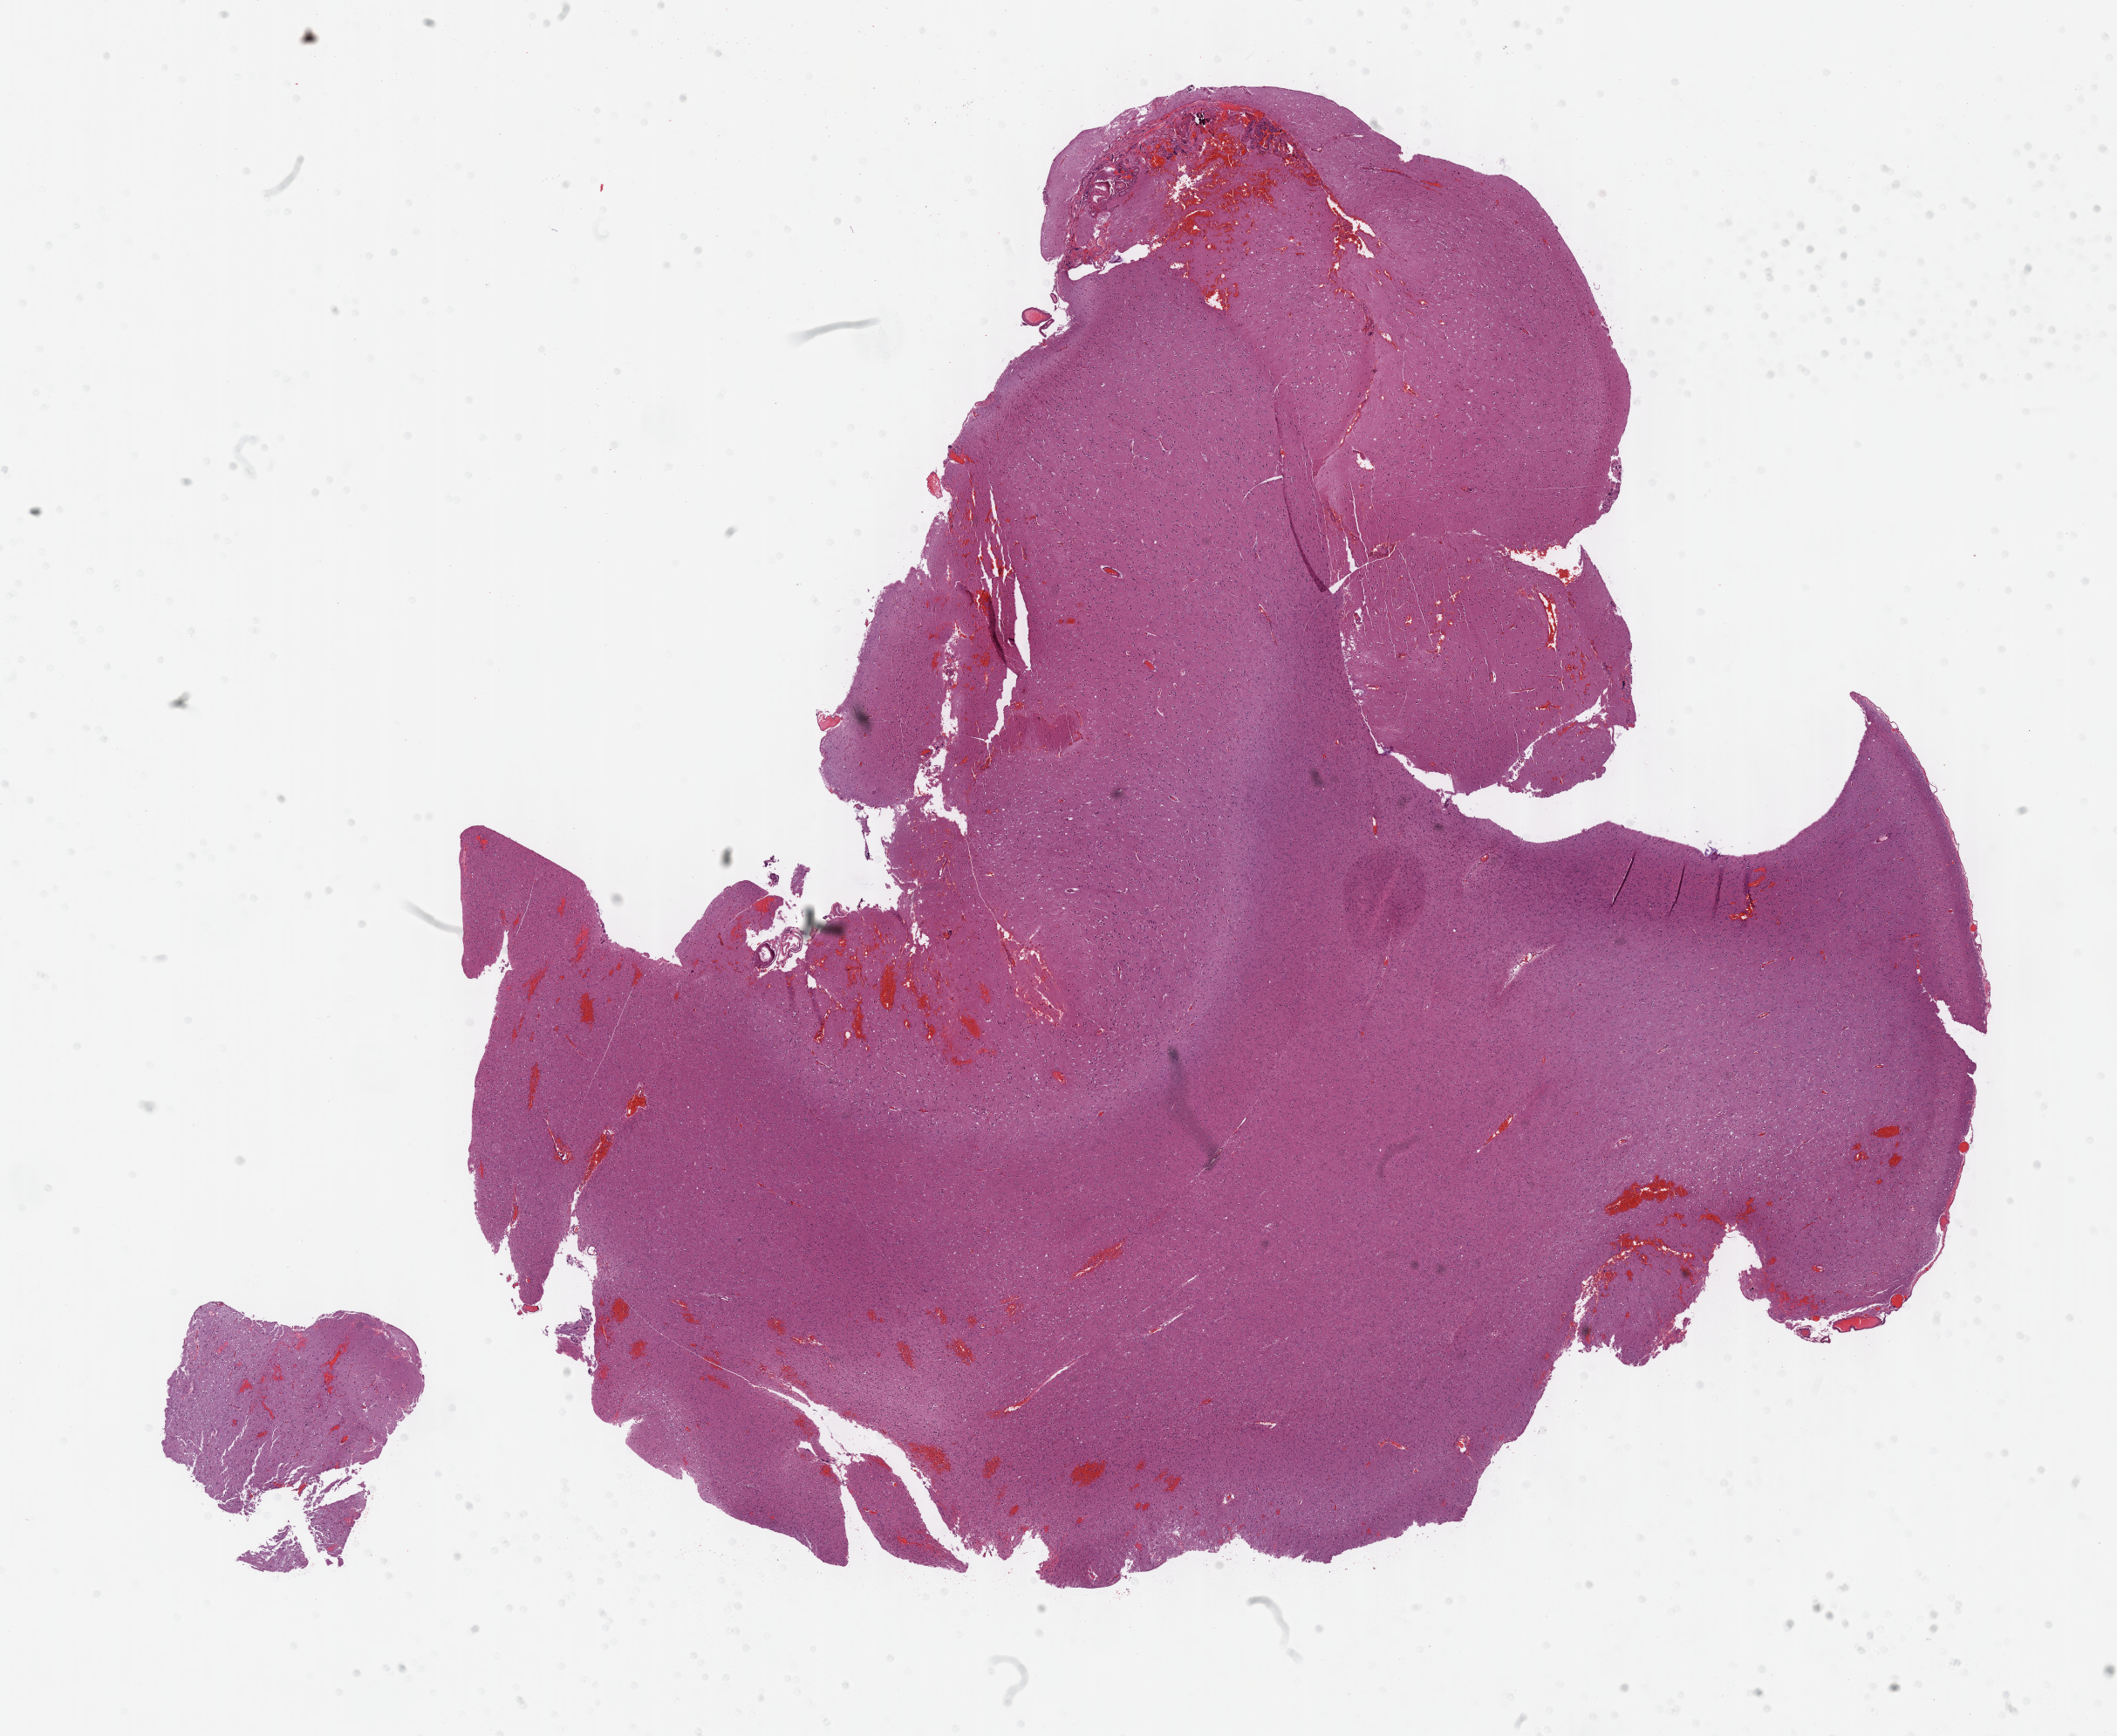
Hematoxylin and eosin (H&E) stained whole-slide image, low-resolution overview of the scanned area, about 19.6 x 16.1 mm (from a 40x scan), formalin-fixed paraffin-embedded (FFPE) diagnostic section, primary tumour sample from the brain. Male patient; age at initial diagnosis 37 years. Histologic grade: G3 (poorly differentiated).
Histologic diagnosis: Oligodendroglioma, anaplastic.